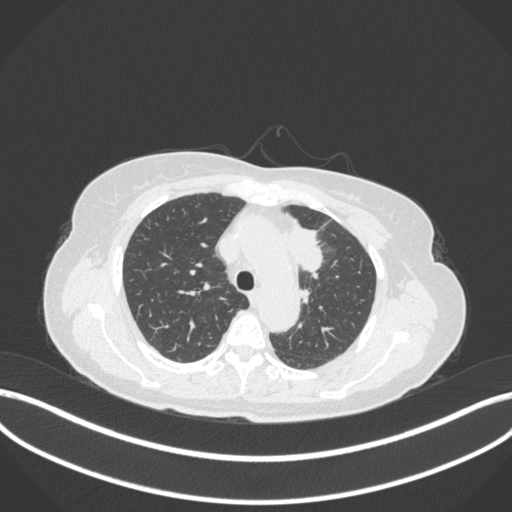
Chest CT, one axial slice; slice 243 of 368 in the series (ordered by position); reconstruction kernel B31f; lung window (W 1500 / L -600 HU); 1 mm slice thickness; 512 × 512 image matrix, field of view 400 × 400 mm. Female patient, age 65 years. Case-level facts recorded for this patient, not image findings: clinical TNM (as recorded): T2a N0 M0.
Structures marked on this image (rectangle marked by the reading radiologist):
- lung tumour (recorded histology: adenocarcinoma): bounding box [x1, y1, x2, y2] px = [286, 220, 325, 275]